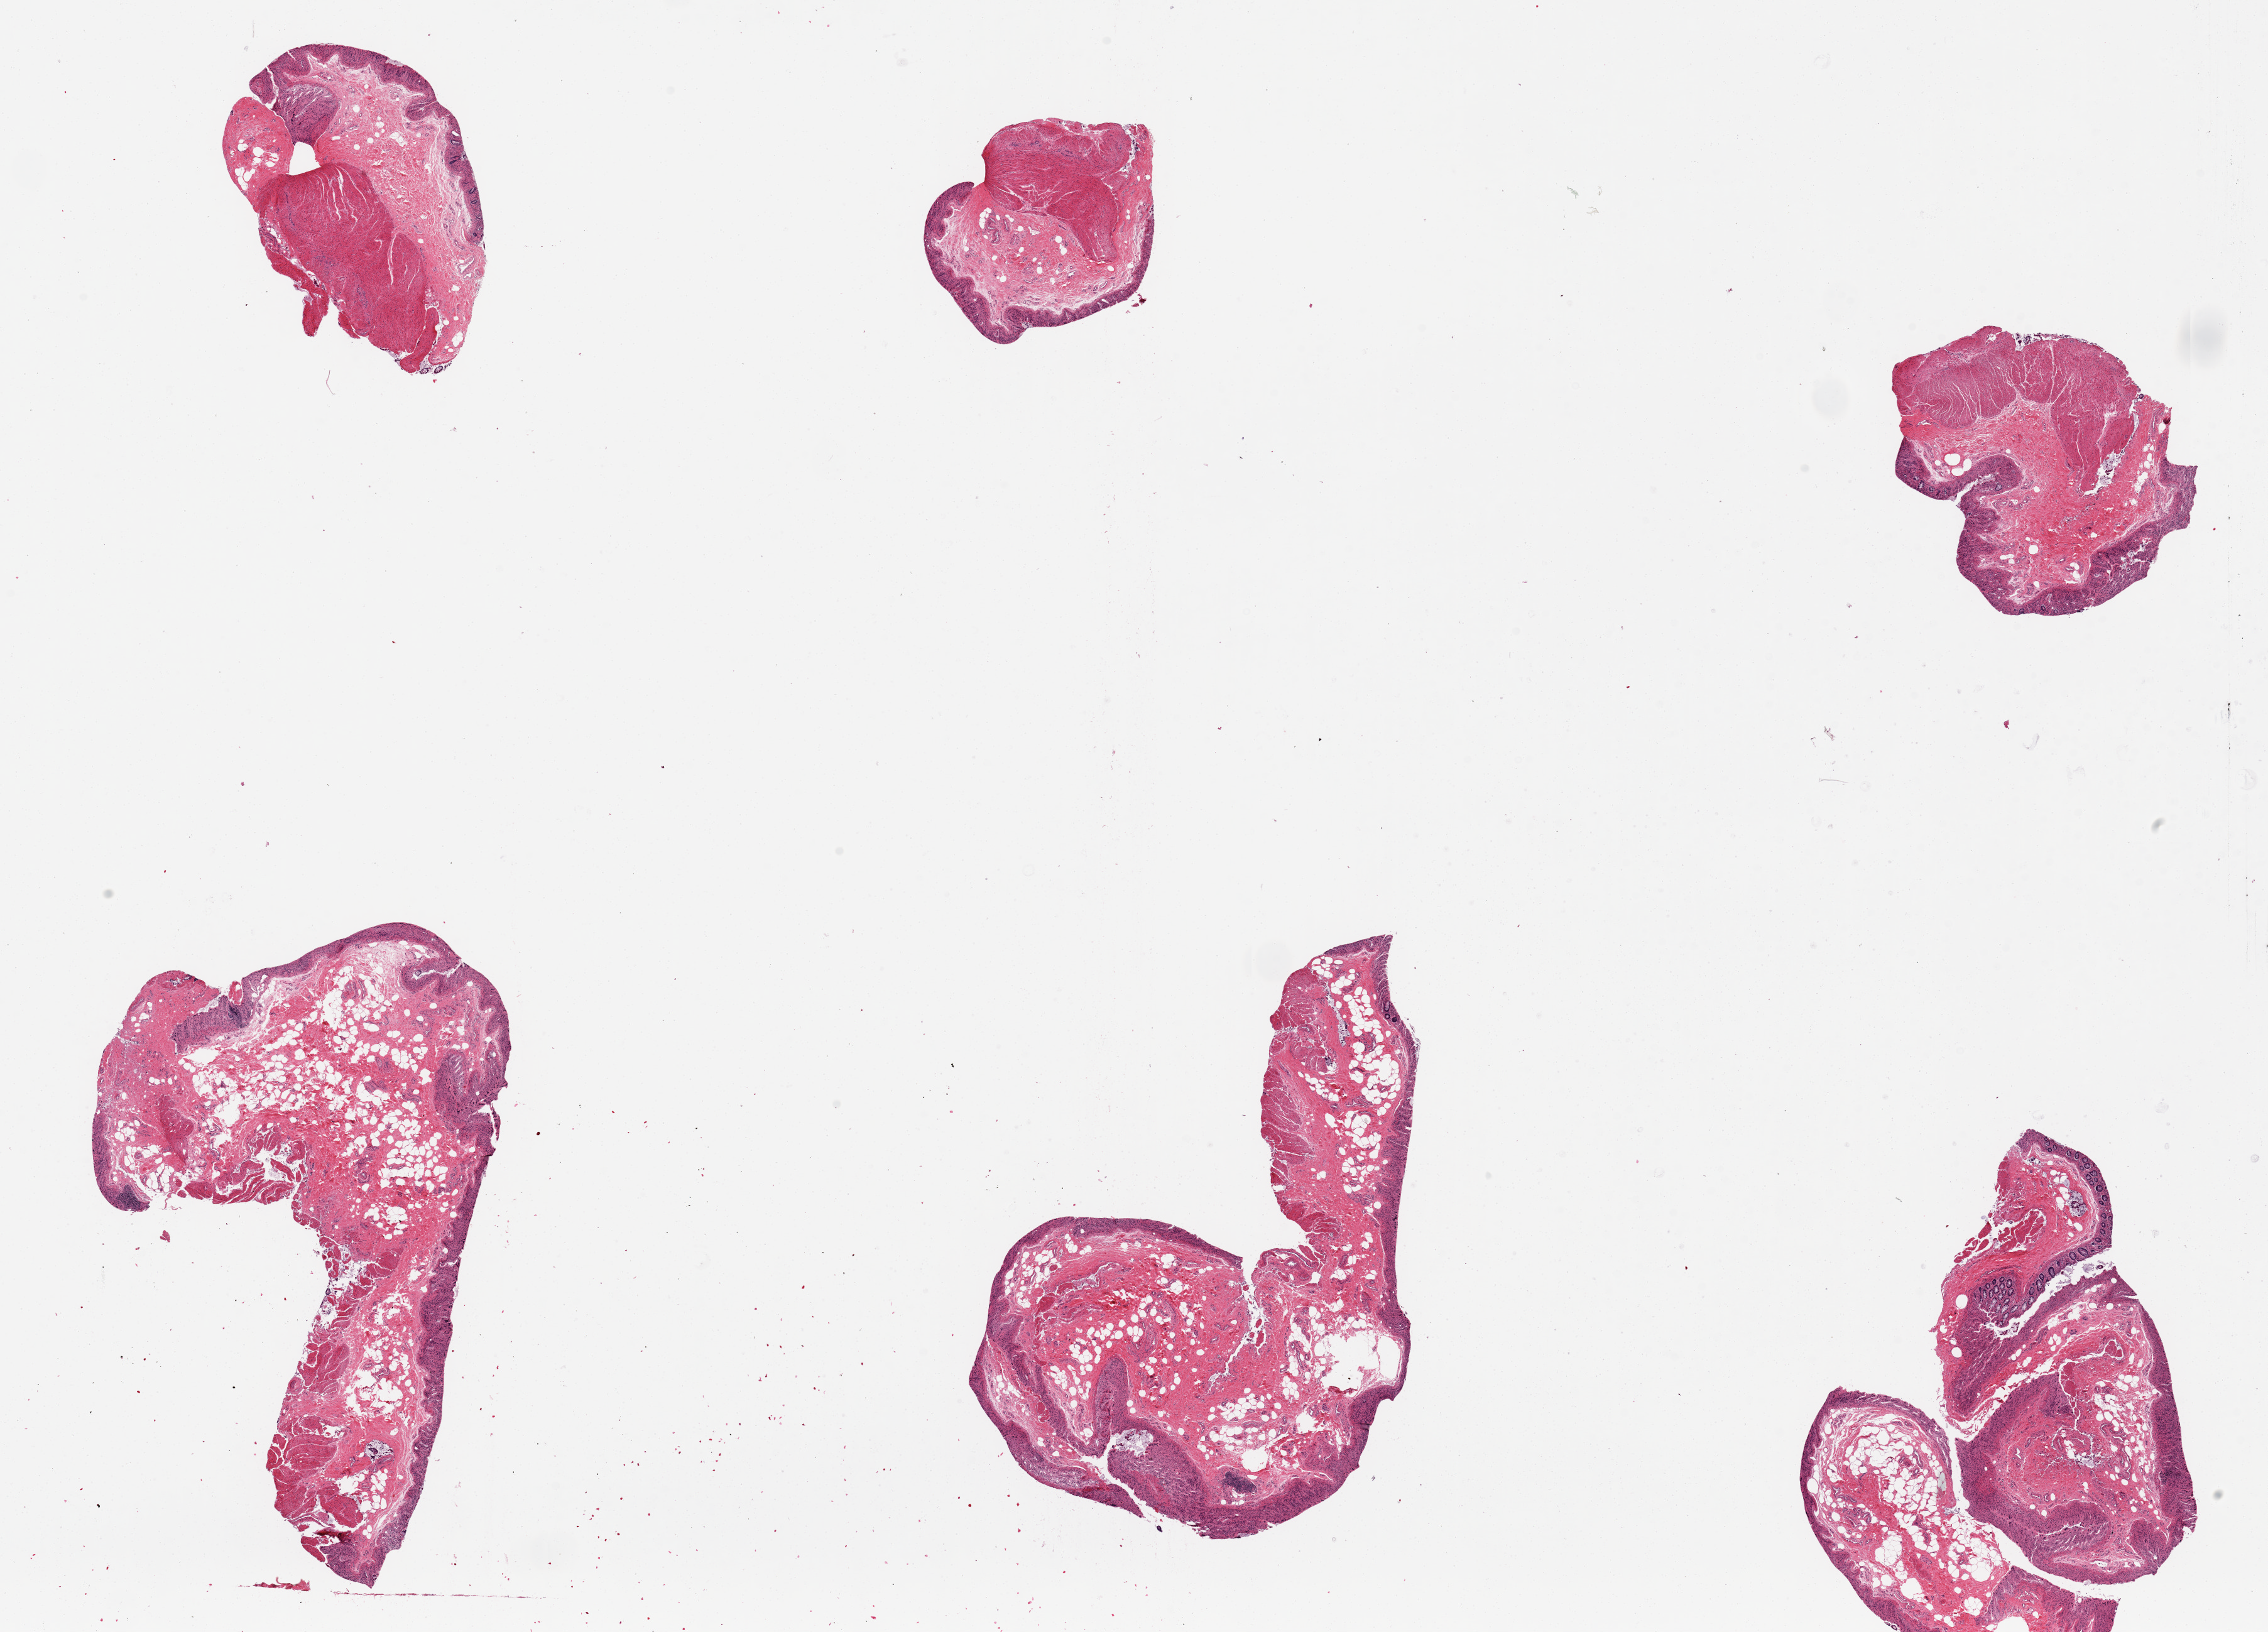
Digitized H&E-stained section — a low-resolution overview of the entire scanned area, about 28.5 x 20.5 mm (slide scanned at 20x). PAXgene-fixed paraffin-embedded (PFPE) section. Section of sigmoid colon (target tissue). Donor tissue sample.
Reviewer comment on this tissue sample: 6 pieces, up to 8x5mm; all have mucosa (autolysis=3) not target; 3 have (target) muscularis (autolysis=2).